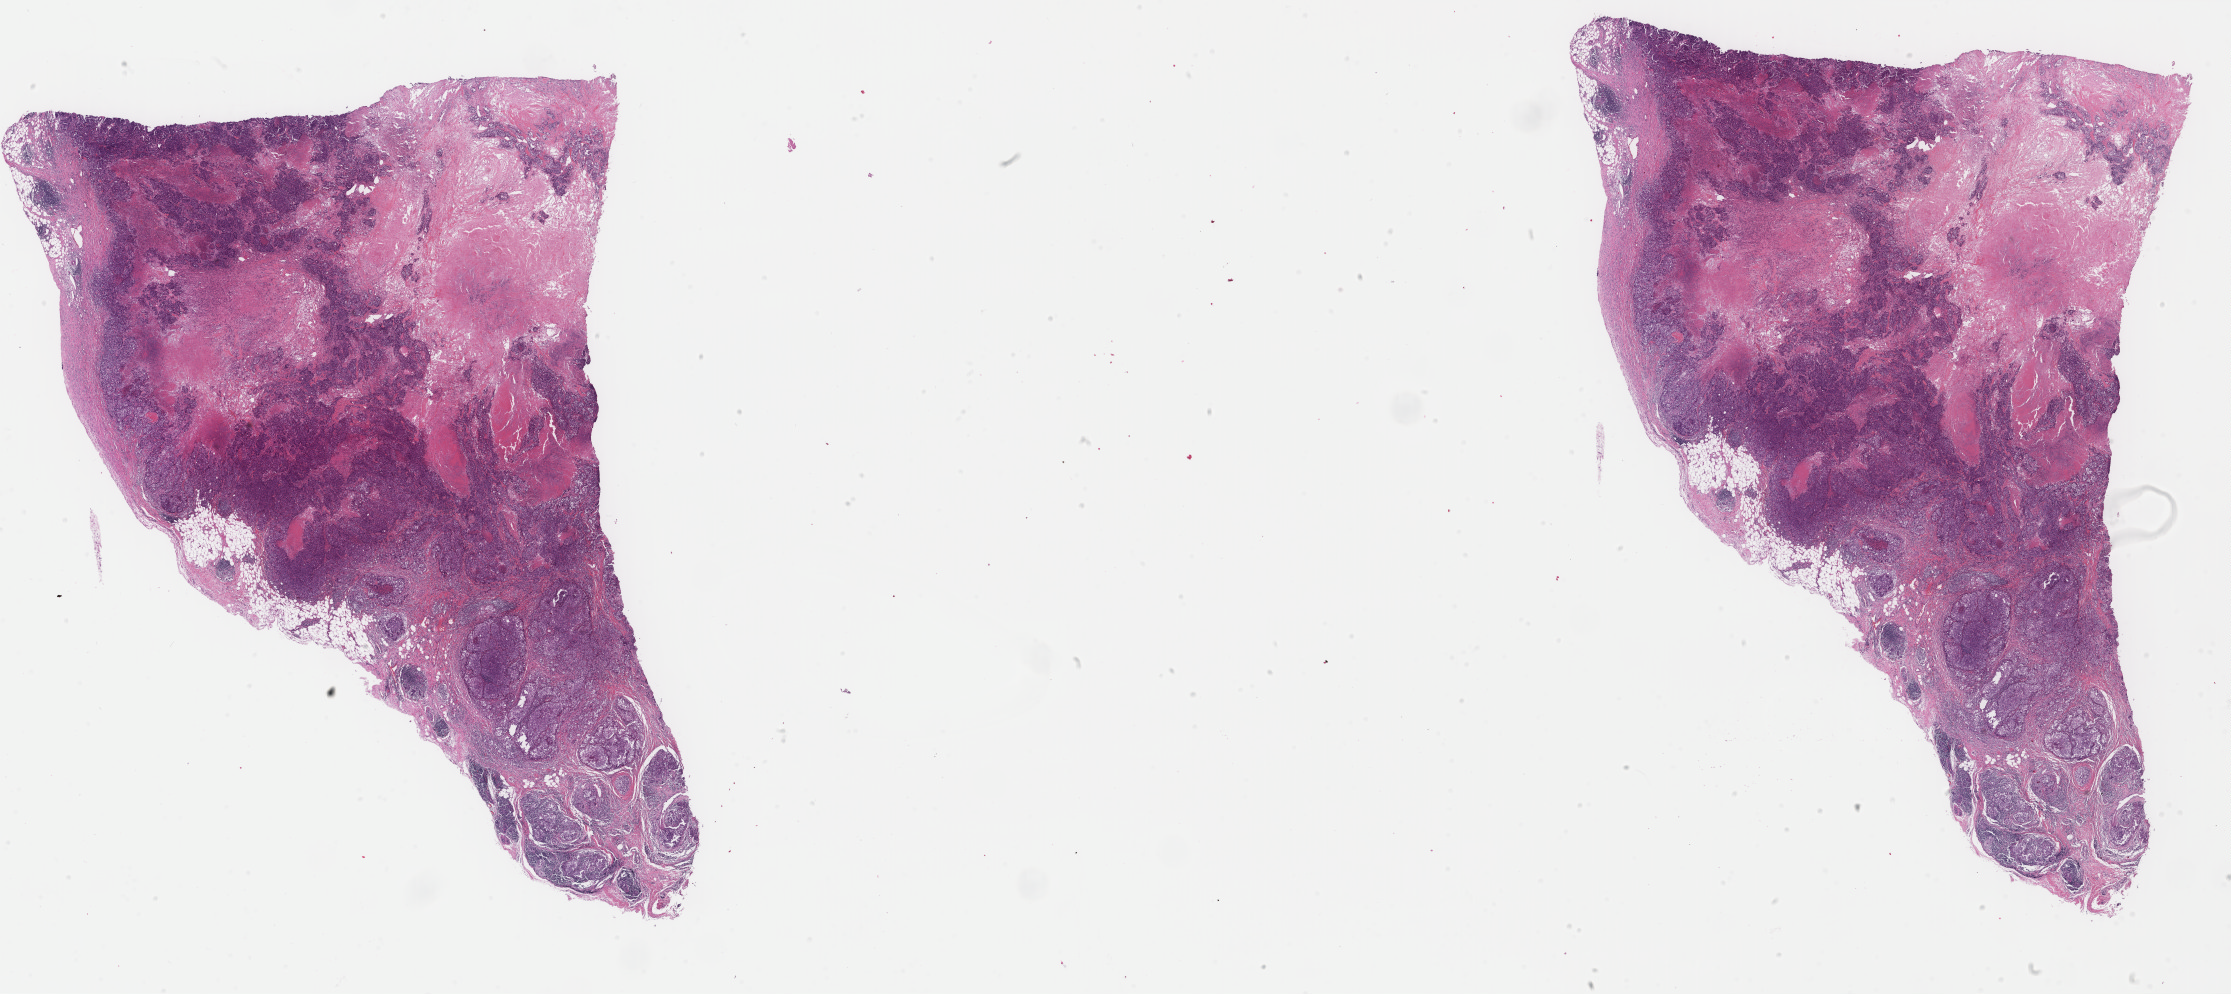
Digitized Hematoxylin and eosin (H&E) stained tissue section (whole slide) — shown as a low-resolution overview of the whole scanned area (about 35.4 x 15.8 mm, from a 40x scan), formalin-fixed paraffin-embedded (FFPE) diagnostic section, primary tumour sample from the breast. Patient: female, age at initial diagnosis 62 years.
AJCC pathologic stage: IIA. Diagnosis: Infiltrating duct carcinoma, NOS. Laterality: right.